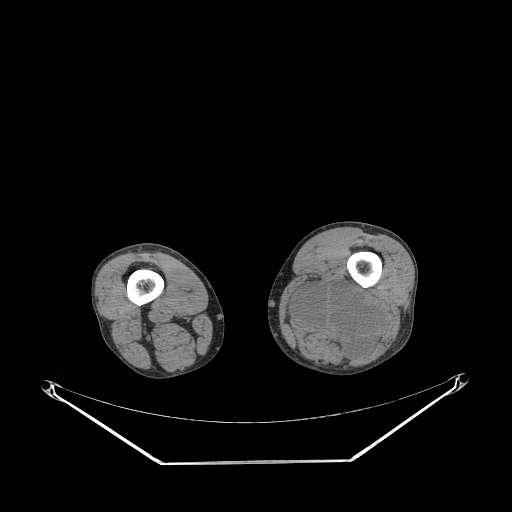
CT of an extremity soft-tissue mass (from a PET/CT study), one axial slice; slice 211 of 267 in the series (ordered by position); 140 kVp; soft-tissue window (W 400 / L 40 HU); 3.75 mm slice thickness; 512 × 512 image matrix, field of view 500 × 500 mm. Male patient. From the clinical record (not read from this slice): histological type: undifferentiated pleomorphic liposarcoma; grade: high; site of the primary tumour: left thigh.
Structures marked on this image (expert contour drawn on MRI and transferred to this co-registered scan by the dataset authors):
- gross tumour volume including surrounding oedema: bounding box (x1, y1, x2, y2) in pixels: (288, 274, 380, 357)
- gross tumour volume (mass): (297, 288, 373, 346)